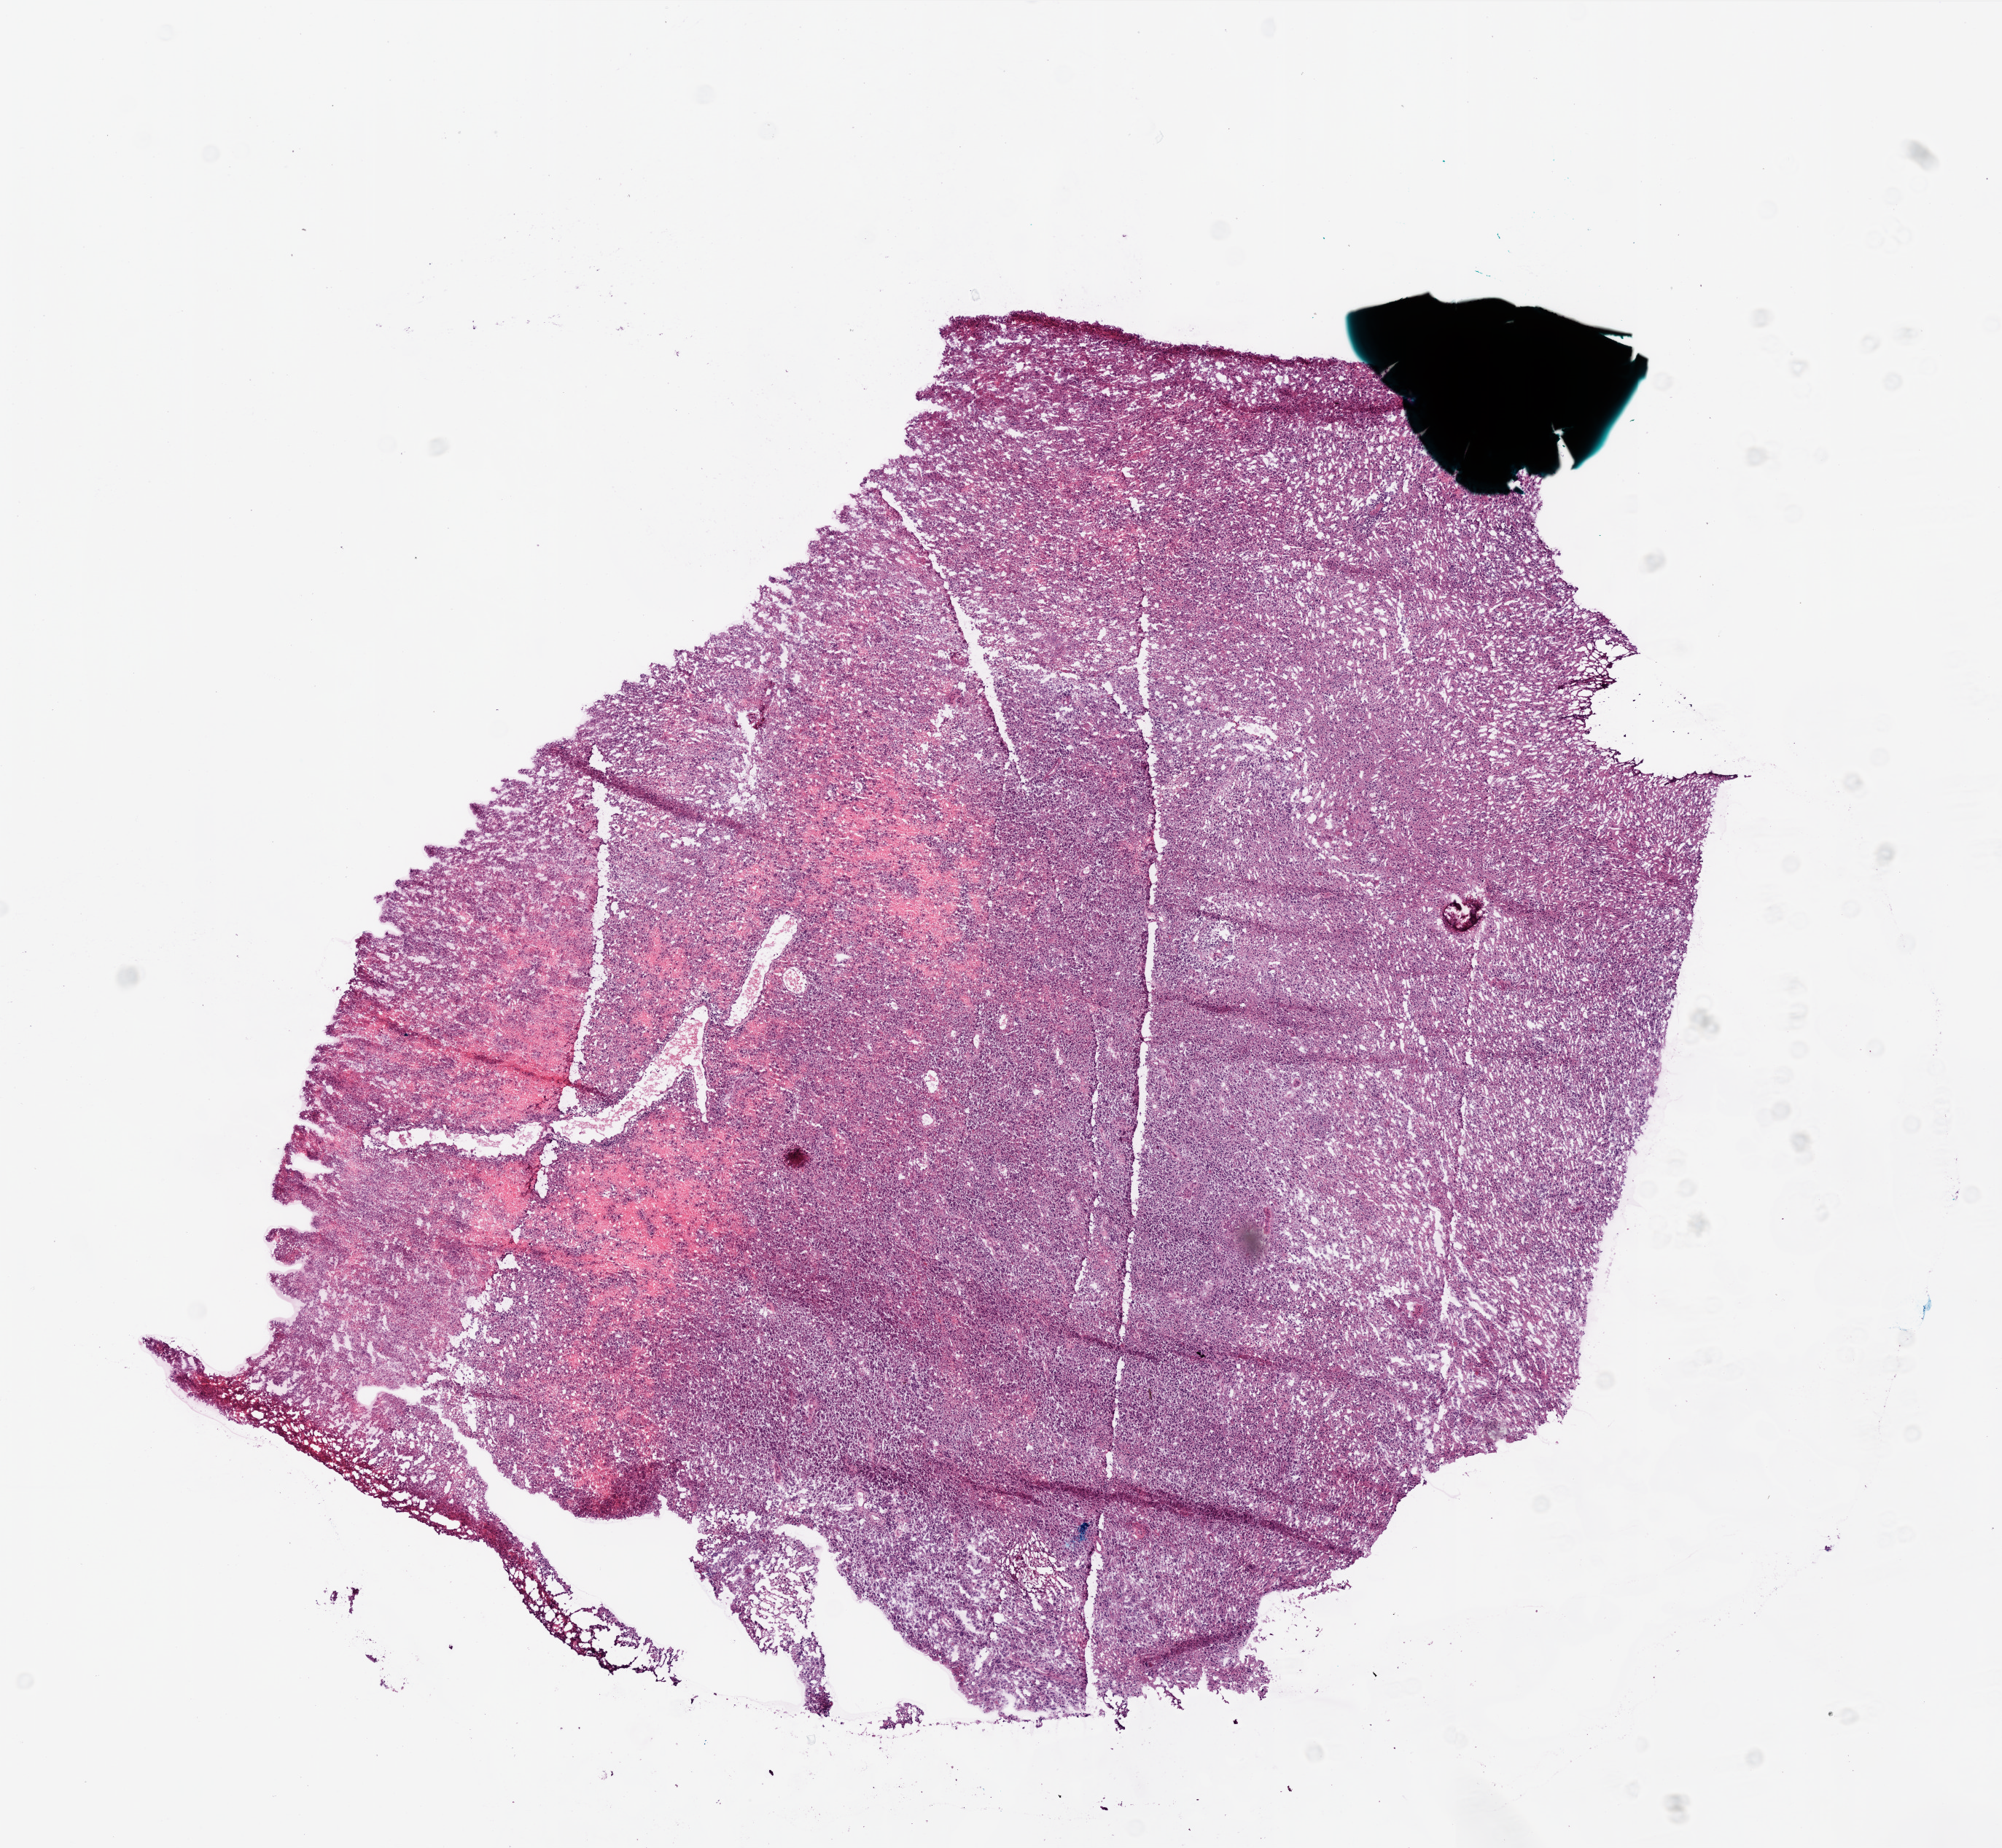
Digitized H&E-stained tissue section (whole slide) — whole scanned area (about 11.0 x 10.1 mm) shown as a low-resolution overview. Frozen section. Brain, primary tumour sample. Patient: female, age at initial diagnosis 83 years. Slide review estimates, as recorded: tumour cells 90%, tumour nuclei 100%, normal cells 0%, stromal cells 0%, necrosis 10%.
Pathologic diagnosis: Glioblastoma.